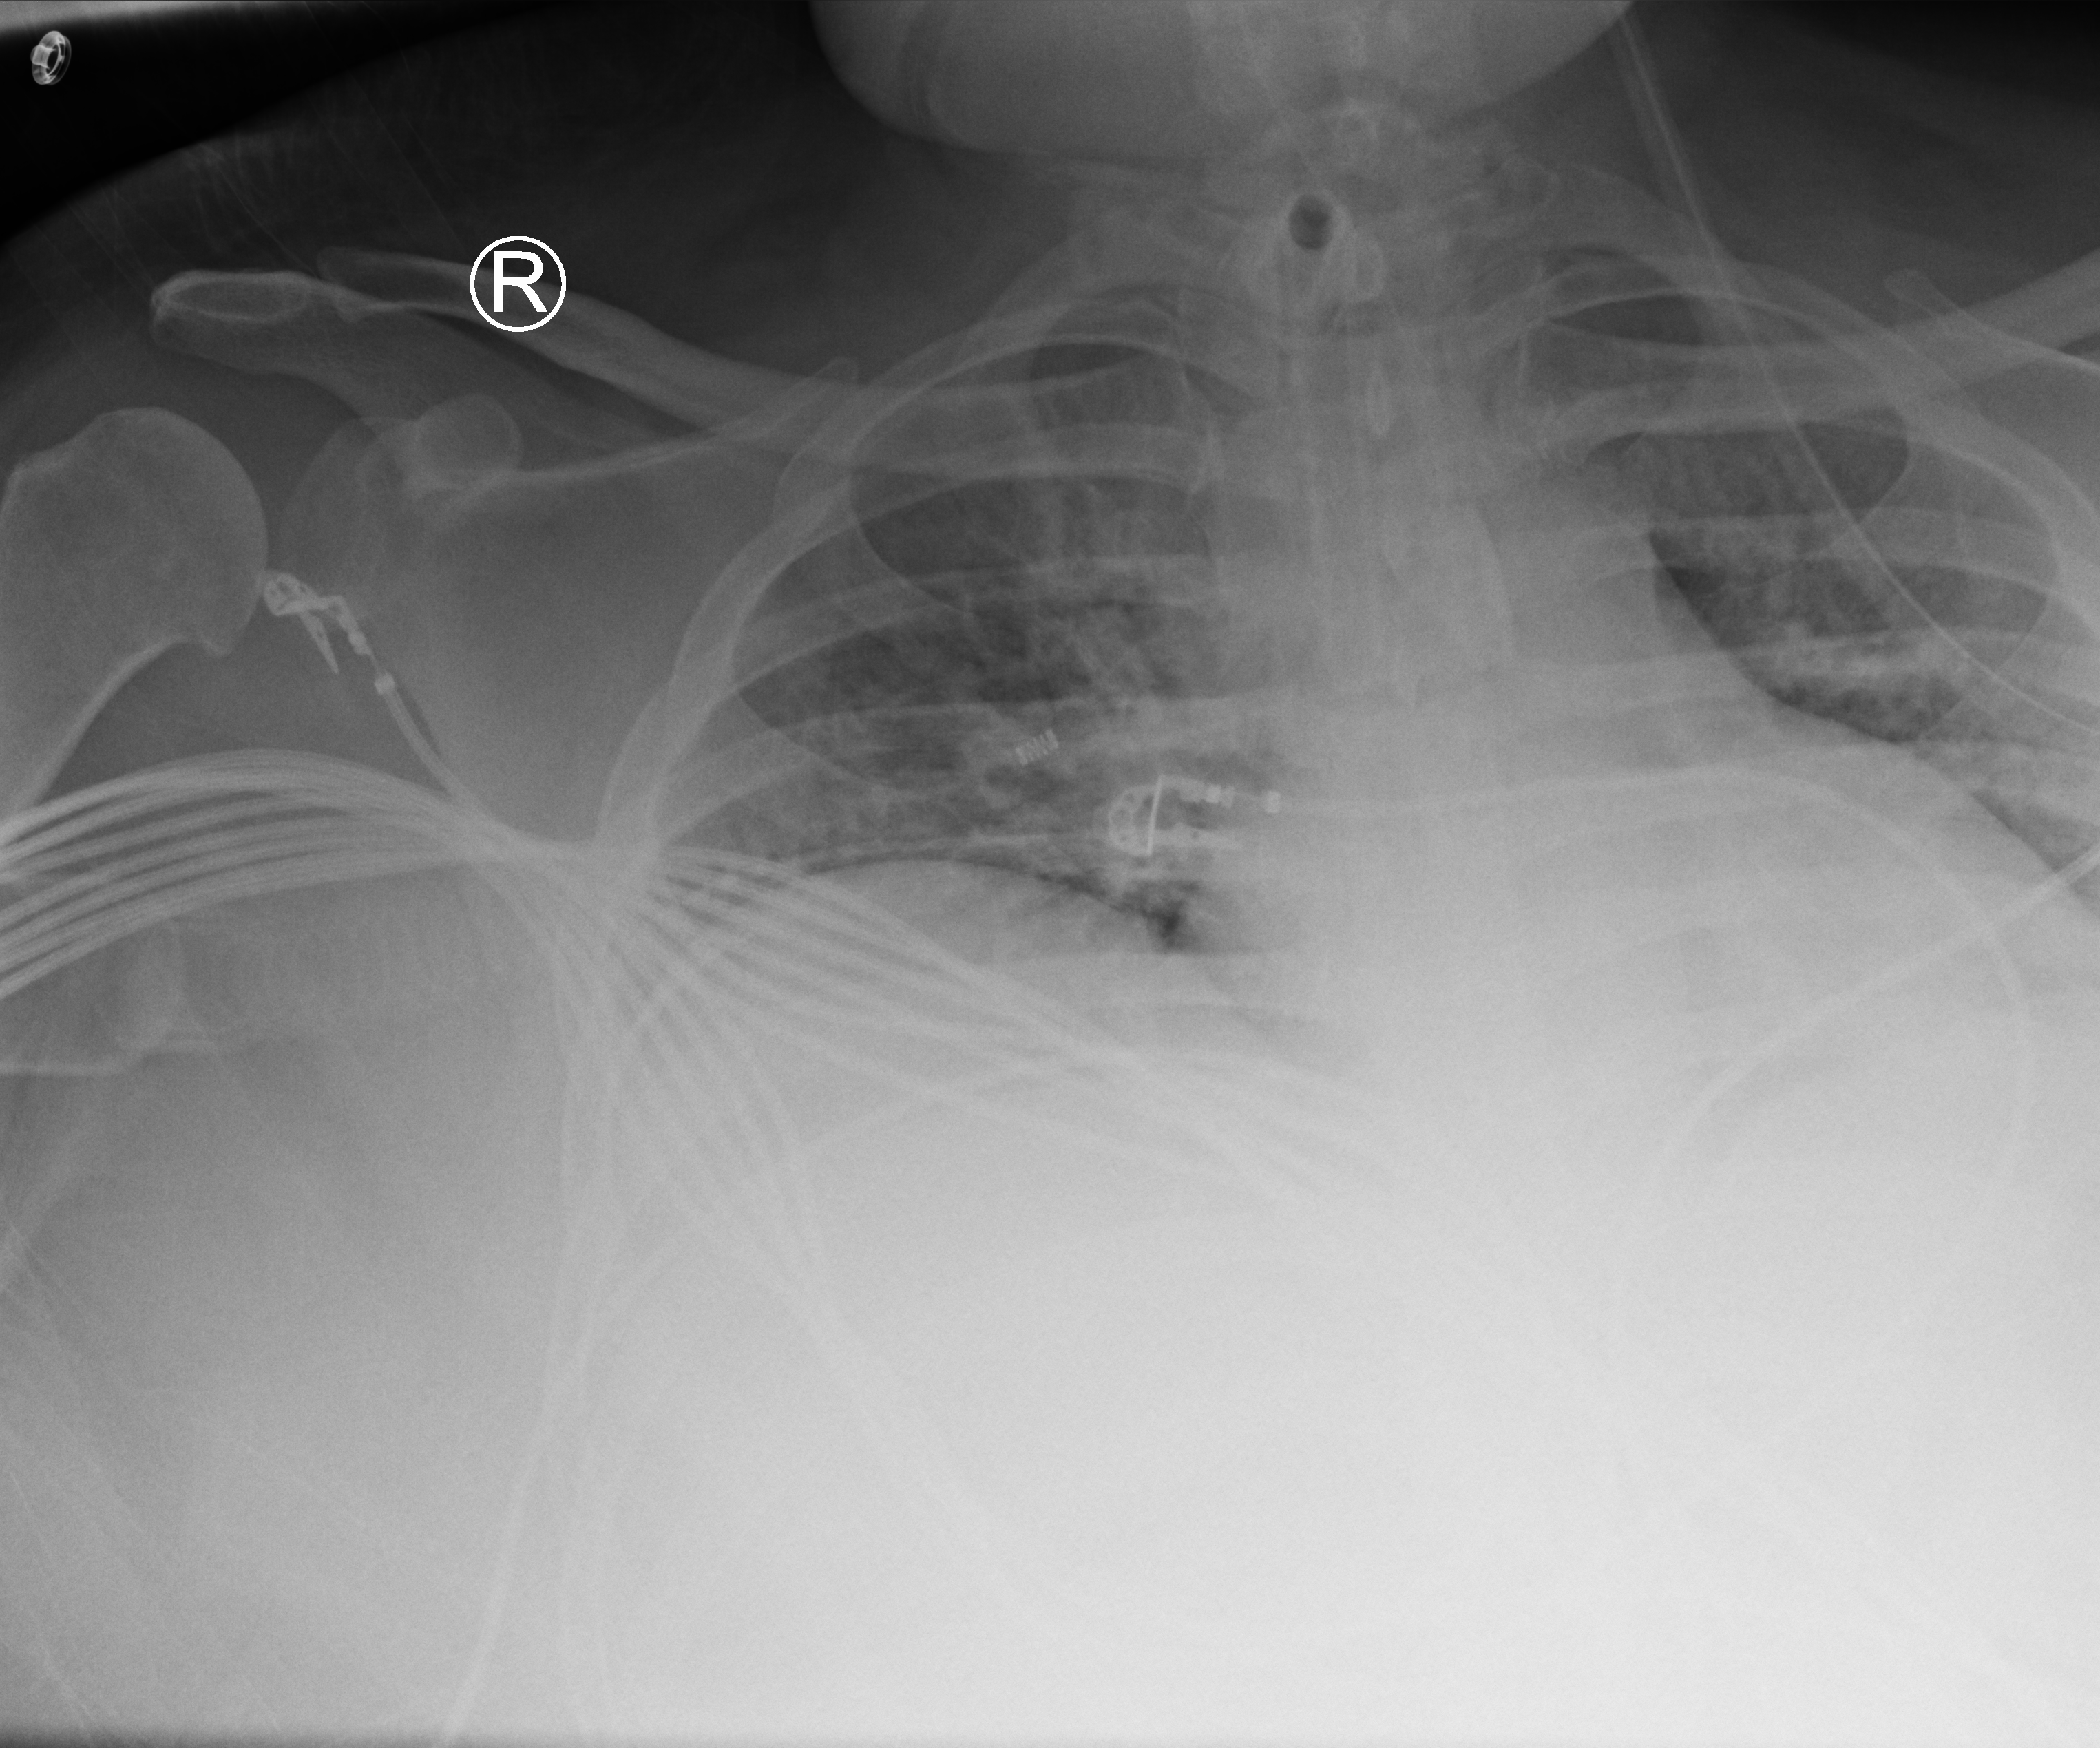
Portable chest radiograph; anteroposterior (AP) projection. Patient hospitalised with COVID-19; male, aged 18–59 years.
From the hospital-stay record, not from the radiograph (when in the stay this image was taken is not recorded): smoking status (admission record): never; mechanically ventilated during this hospital stay: yes; COPD (admission record): yes.